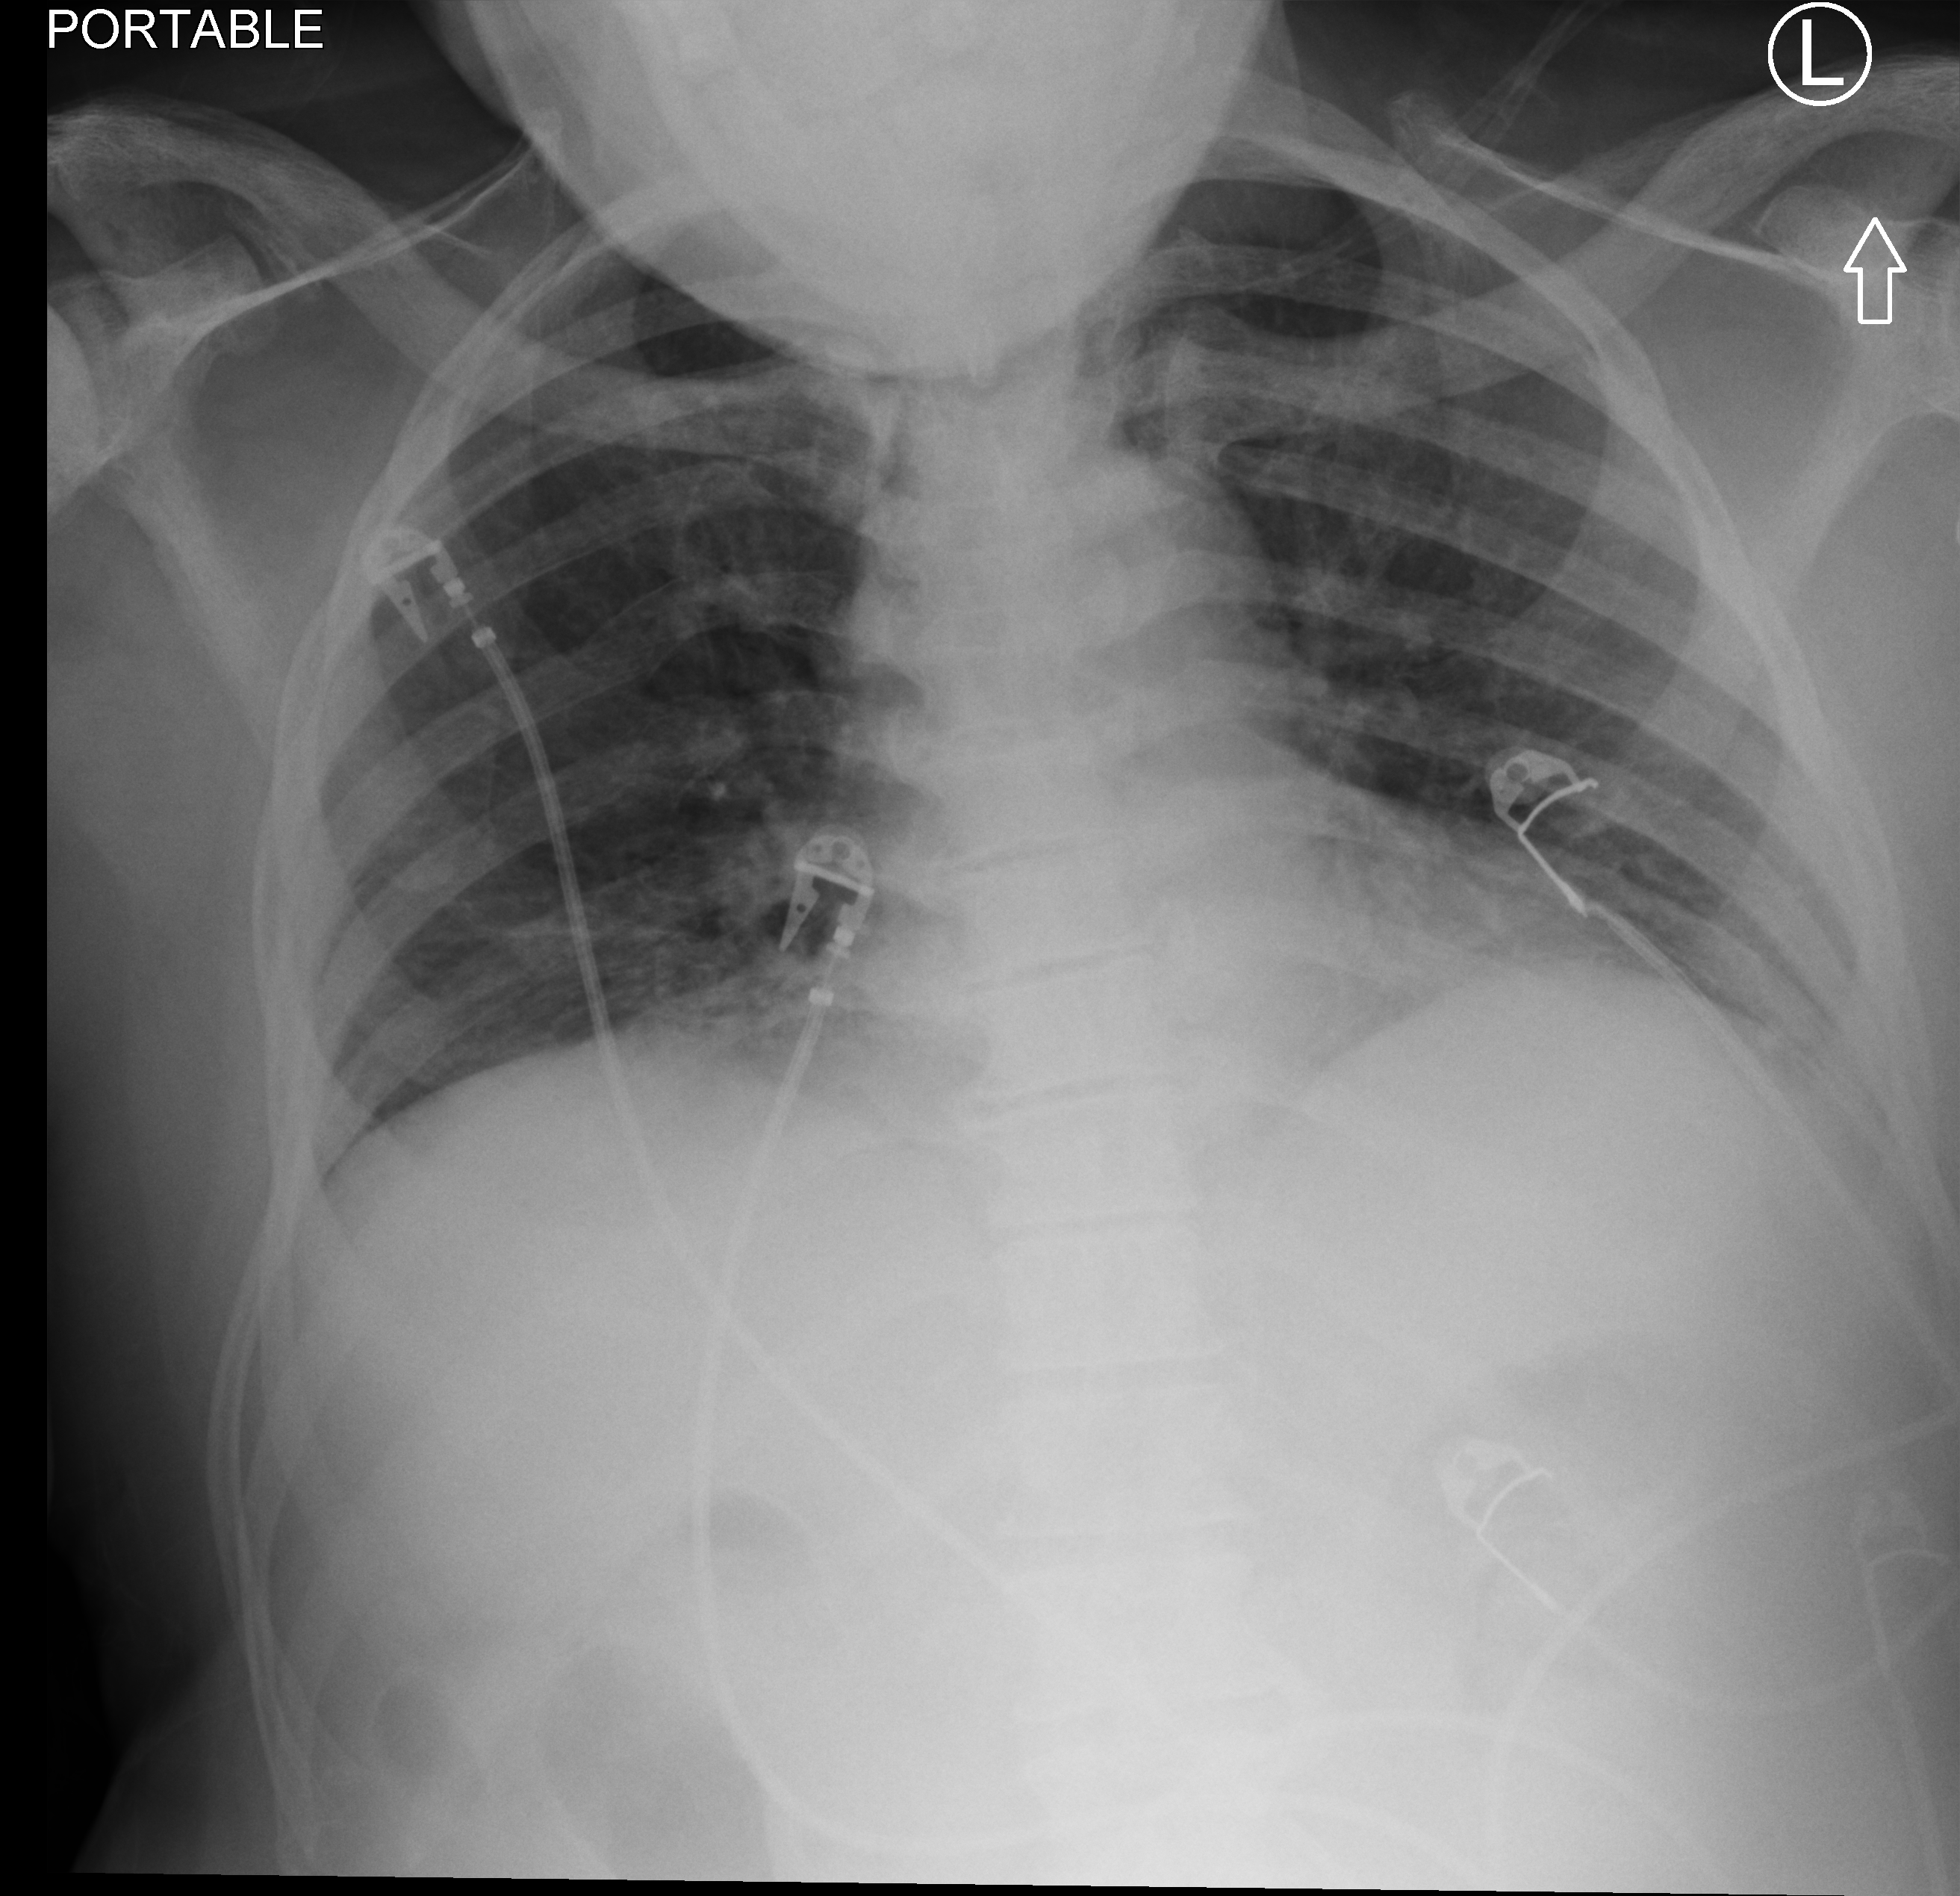
Portable chest radiograph; anteroposterior (AP) projection. Male patient hospitalised with COVID-19, age 60–74 years.
From the hospital-stay record, not from the radiograph (when in the stay this image was taken is not recorded): other chronic lung disease (admission record): no; length of hospital stay: 8 days; COPD (admission record): no.